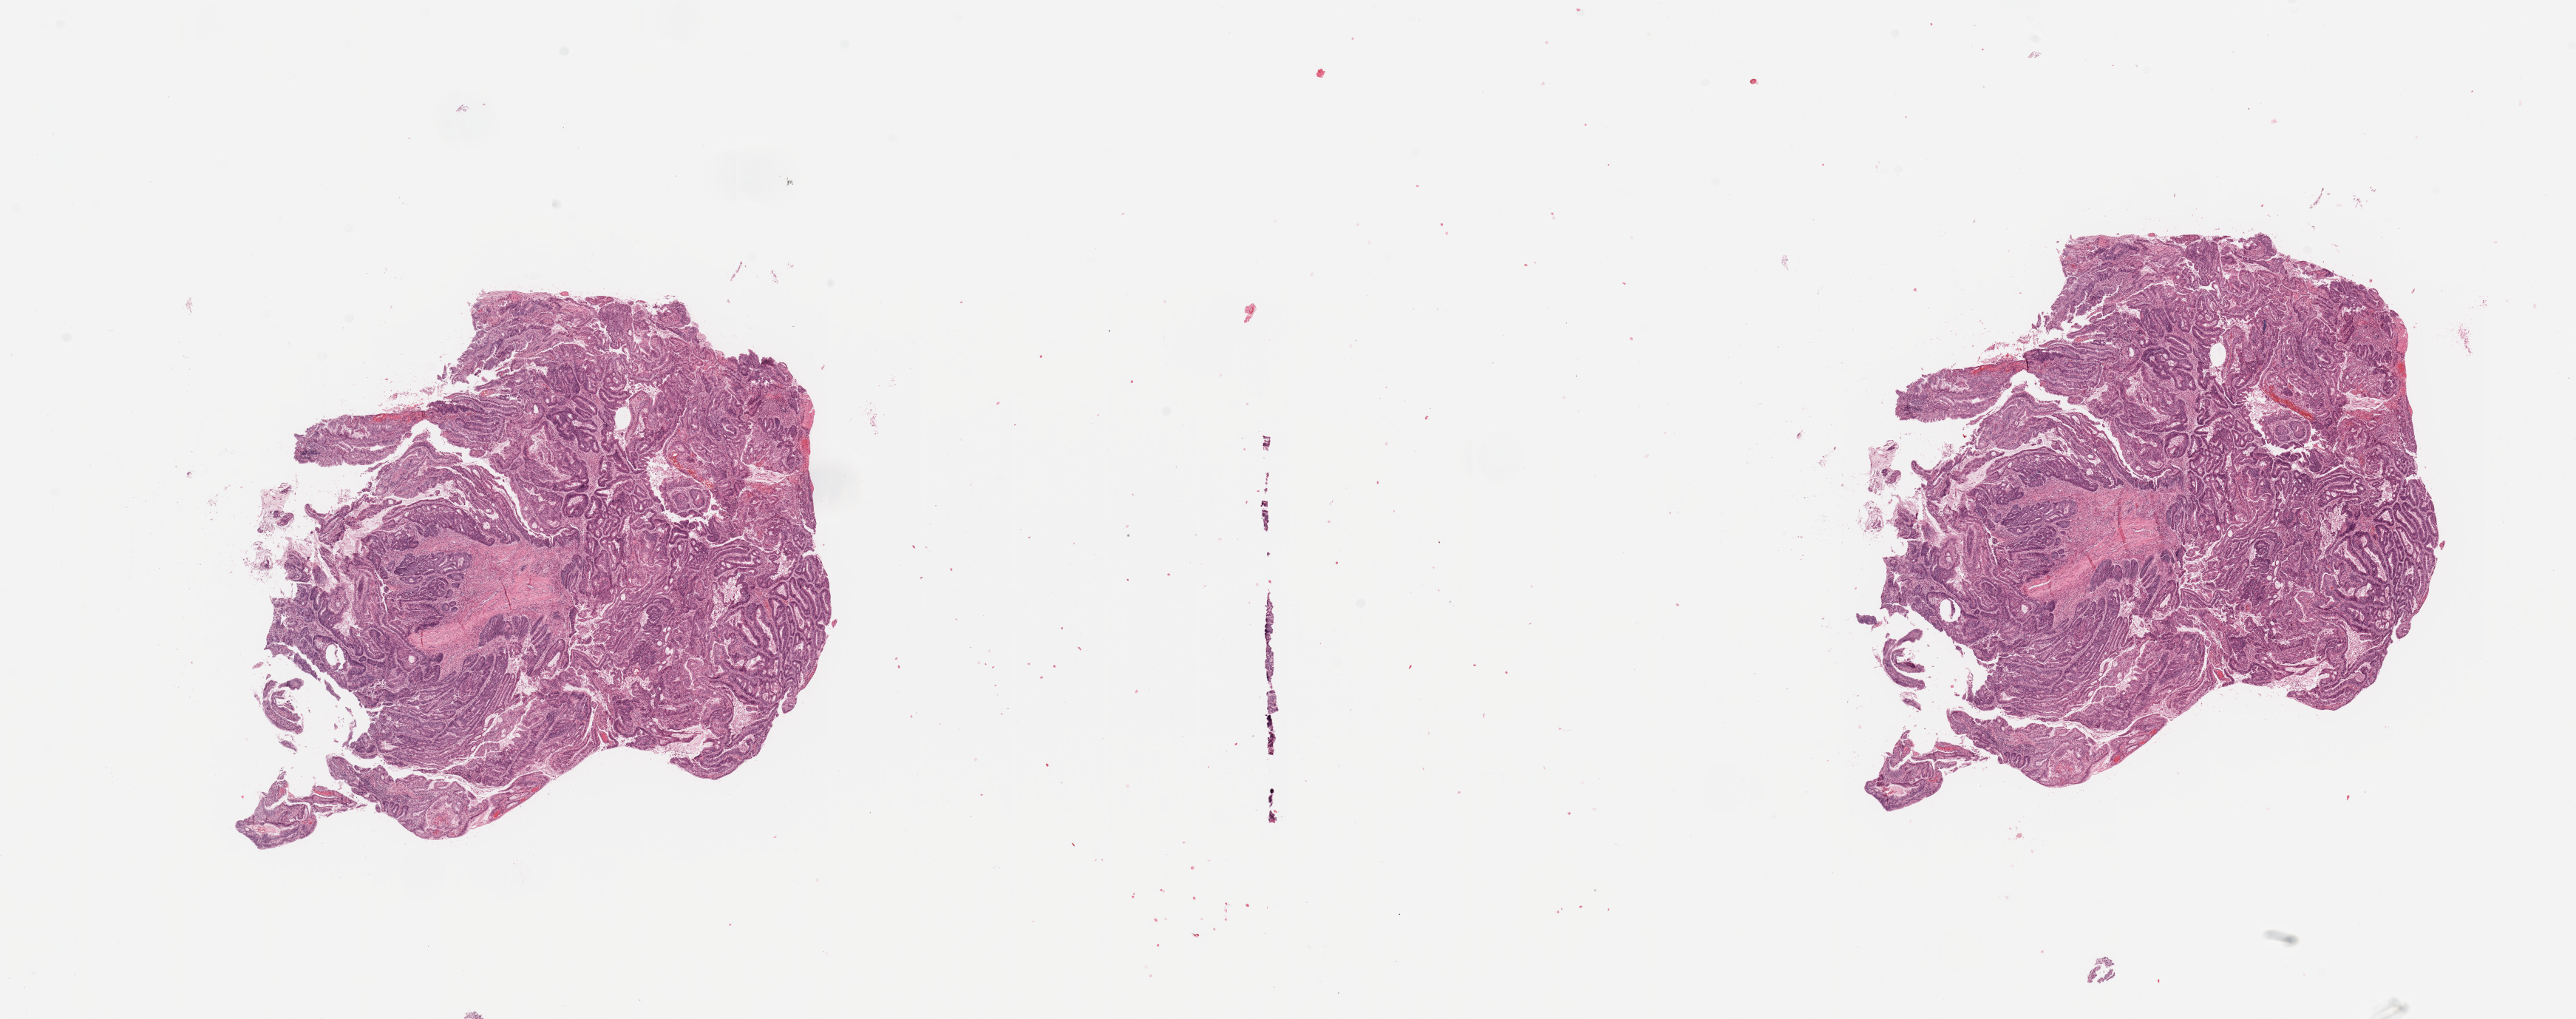
Whole-slide histology image, Hematoxylin and eosin (H&E) stained, a low-resolution overview of the entire scanned area, about 27.6 x 10.9 mm (slide scanned at 20x). Tumour tissue sample, sampled site: uterus. Female, 53 y/o. Histologic grade: G1 (well differentiated). Pathologist review of this section (percent, as recorded): tumour nuclei 85%, necrosis 5%.
AJCC pathologic stage: III. Primary tumour site (as recorded): anterior endometrium. Histologic diagnosis: Endometrioid adenocarcinoma, NOS.